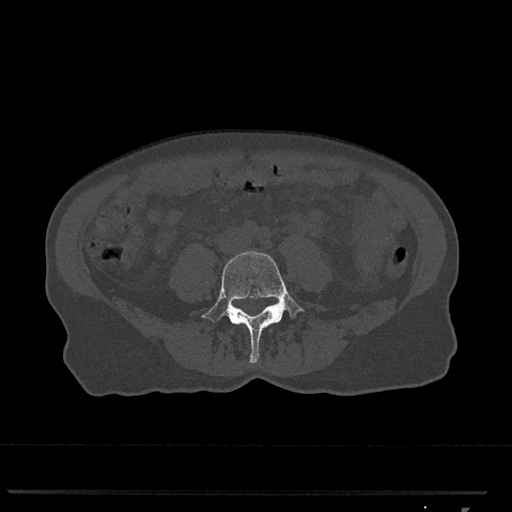
CT including the spine, one axial slice; slice 210 of 793 in the series (ordered by position); reconstruction kernel Br40s/3; 120 kVp; bone window (W 1800 / L 400 HU); 0.5 mm slice thickness; 512 × 512 image matrix. Female patient, age 62 years. Case-level facts recorded for this patient, not image findings: primary cancer: renal.
Outlined on this slice (semi-automatically segmented with operator editing):
- L4 vertebra: bounding box (x1, y1, x2, y2) in pixels: (202, 251, 304, 364)